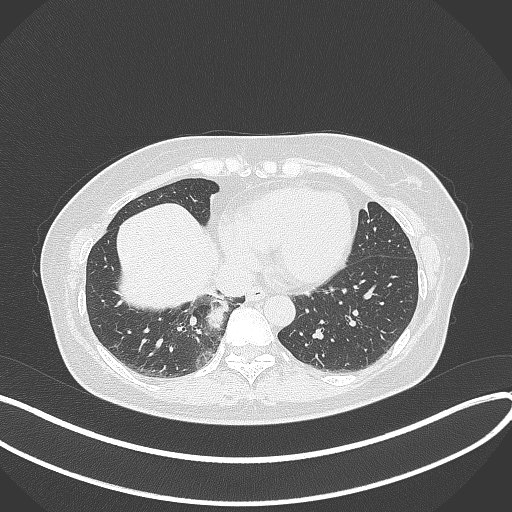
Chest CT, one axial slice. Position 104 of 331 along the scan axis. Reconstruction kernel B70f. 120 kVp. Lung window (W 1500 / L -600 HU). 1 mm slice thickness. 512 × 512 image matrix, field of view 400 × 400 mm. Female patient, age 54 years. Case-level facts recorded for this patient, not image findings: clinical TNM (as recorded): T4 N0 M0.
Annotated regions visible in this slice (rectangle marked by the reading radiologist):
- lung tumour (recorded histology: adenocarcinoma): bounding box <206,294,232,338> (left, top, right, bottom; pixels)